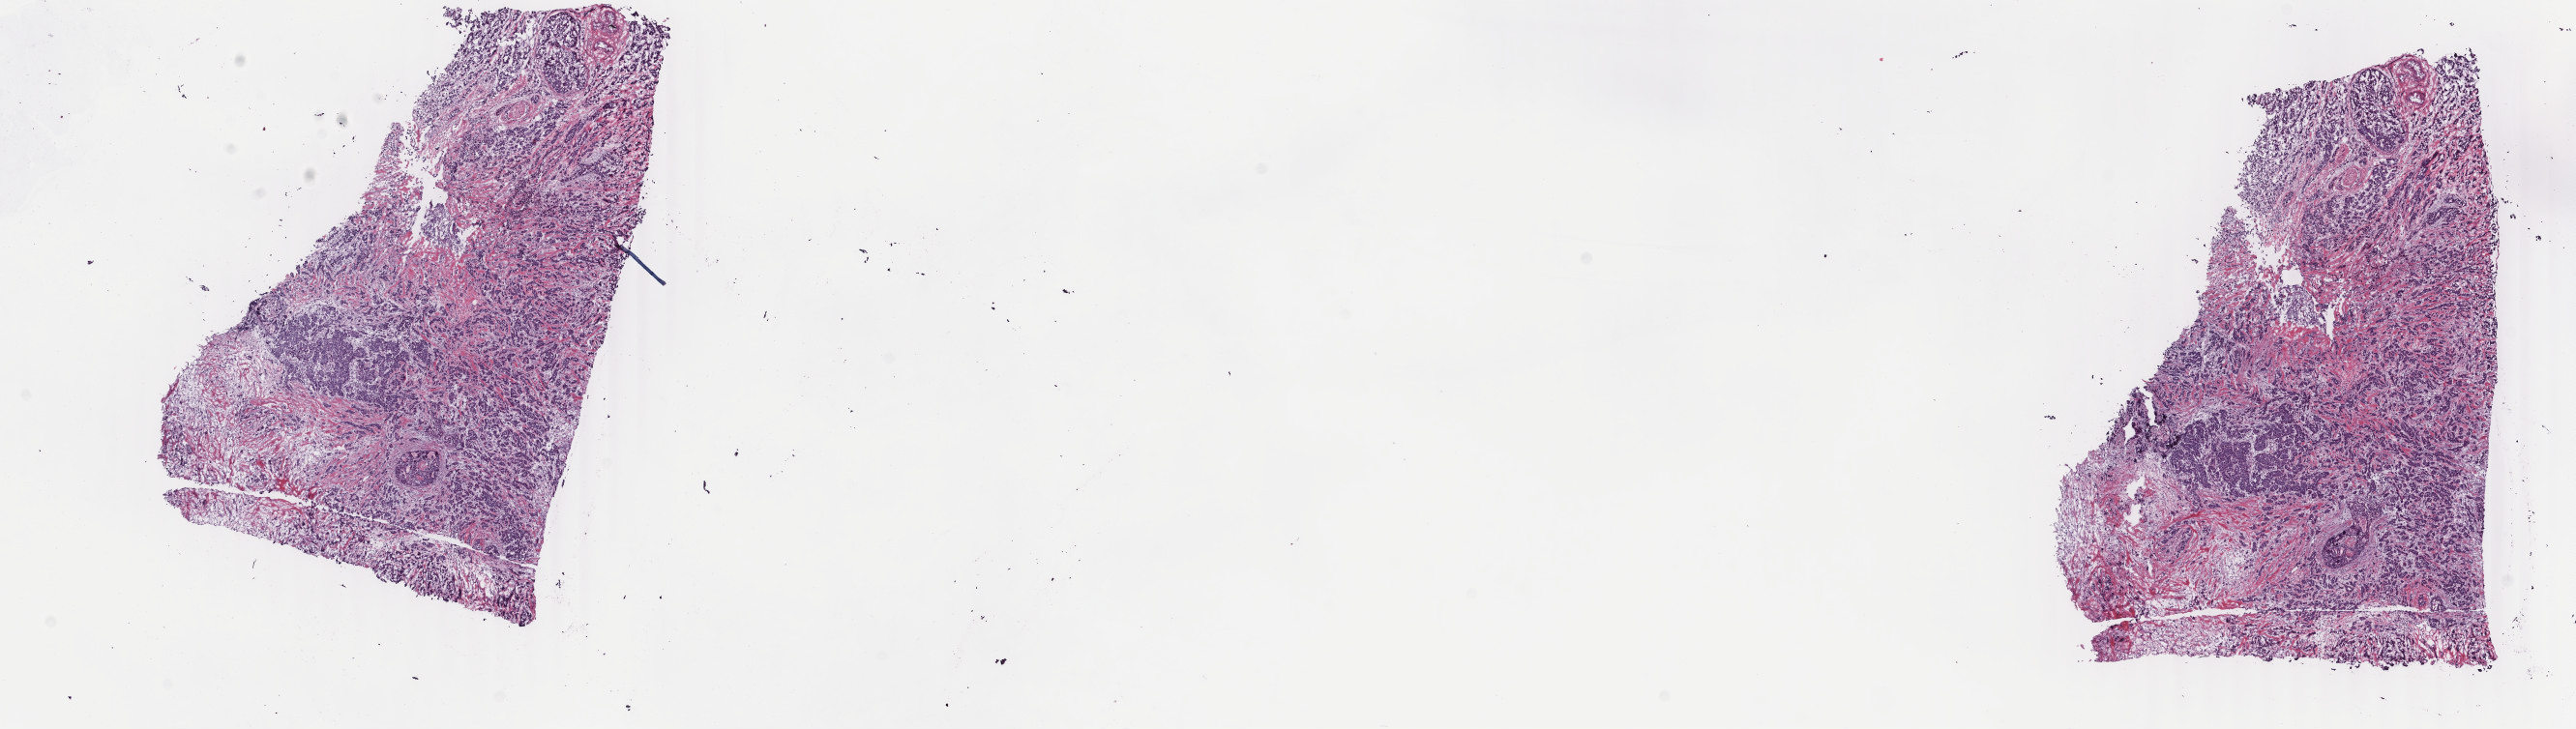
Digitized H&E tissue section (whole slide), low-resolution overview of the scanned area, about 21.2 x 6.0 mm (from a 40x scan); frozen section; sample: primary tumour, breast. Female patient; age at initial diagnosis 52 years. Pathologist review of this section (percent, as recorded): tumour cells 65%, tumour nuclei 85%, normal cells 0%, stromal cells 35%, necrosis 0%. Inflammatory infiltration, as recorded: lymphocyte infiltration 1%, monocyte infiltration 0%, neutrophil infiltration 0%.
AJCC pathologic stage: IIB. Pathologic diagnosis: Infiltrating duct carcinoma, NOS. Lymph nodes positive (case pathology): 1 of 2 examined. Laterality: right.